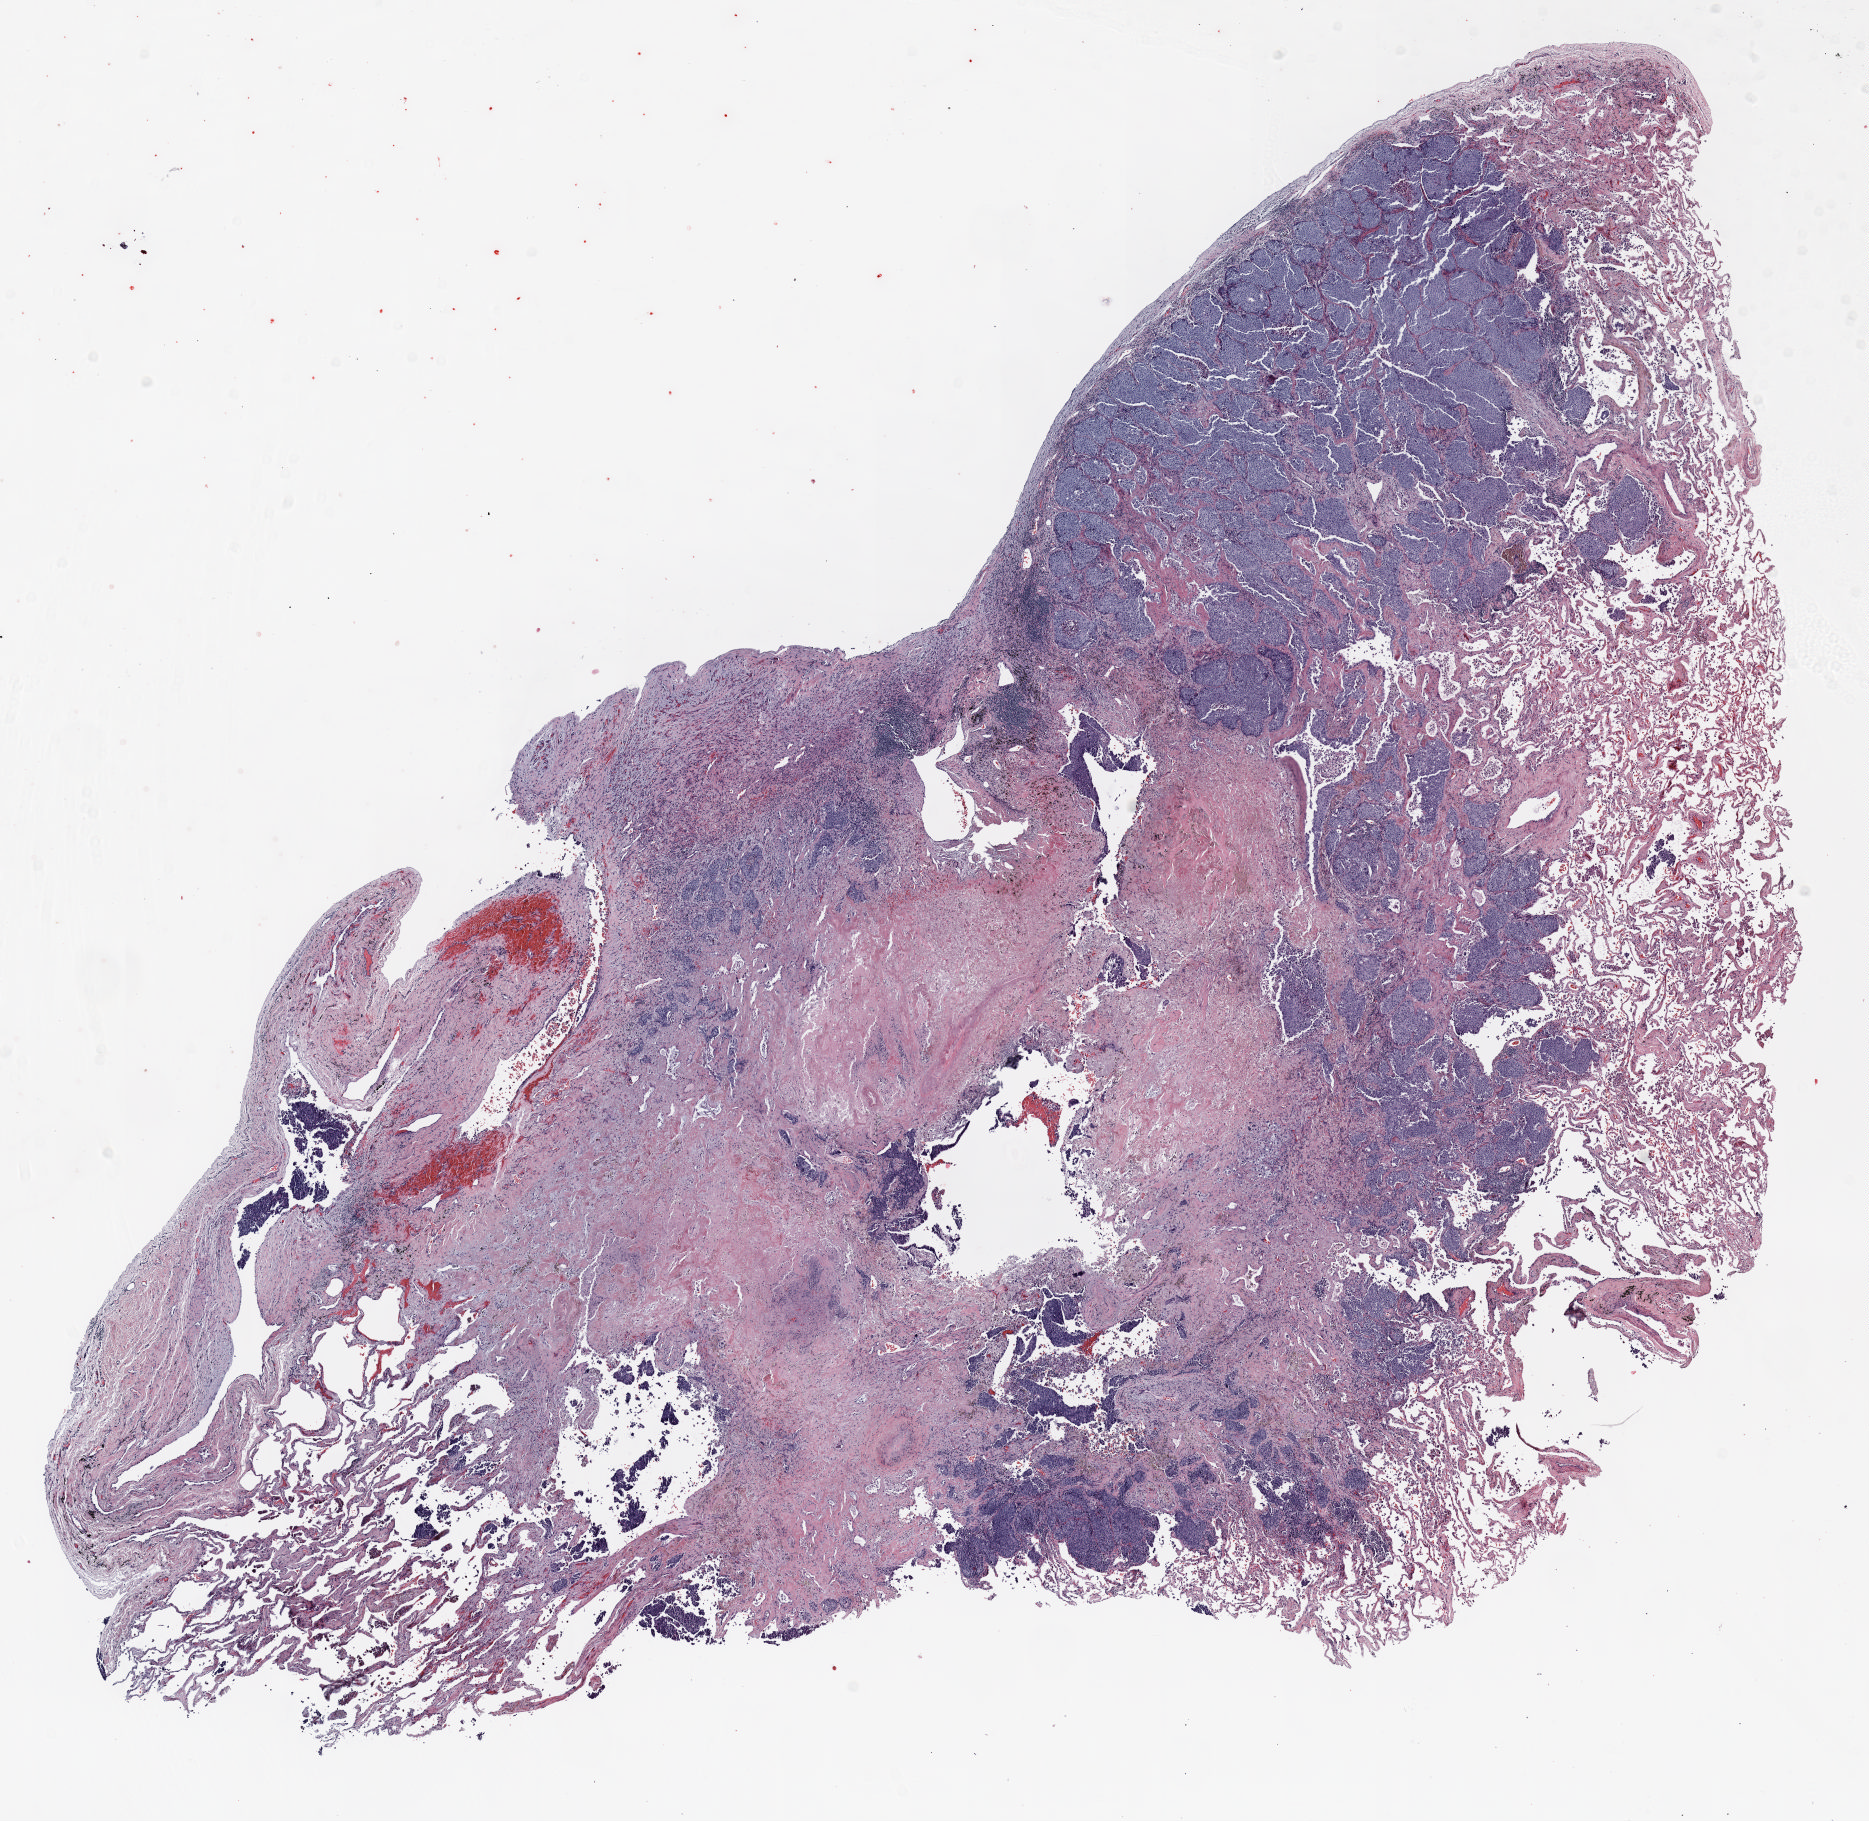
Hematoxylin and eosin (H&E) stained whole-slide image — a low-resolution overview of the entire scanned area, about 15.0 x 14.6 mm; FFPE section; lung. Male patient, aged 64 at enrolment. Current smoker at enrolment. Grade: poorly differentiated (G3).
Primary tumour location (clinical record): right upper lobe. Participant's lung-cancer diagnosis: Adenocarcinoma, NOS (ICD-O-3 8140/3). Stage (AJCC 6th edition): IA. Tumour size (pathology): 13 mm.